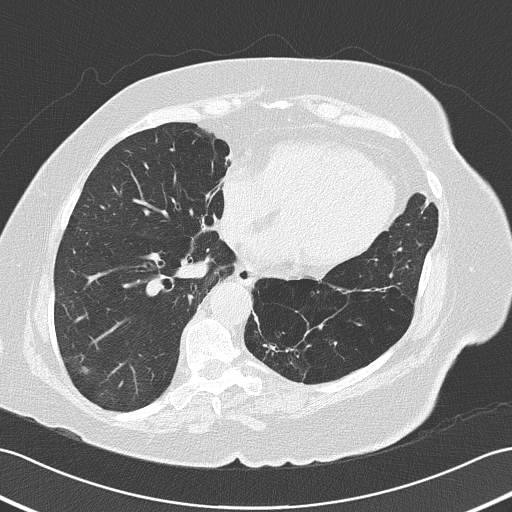
Chest CT (low-dose screening protocol), one axial image, first (baseline) screen, lung window (W 1500 / L -600 HU), 2 mm slice thickness, 512 × 512 image matrix, field of view 353 × 353 mm. Female, age 73 years at enrolment.
- Expert-annotated lung lesion, box from (x=55, y=339) to (x=101, y=388) px.
- The screening reader recorded 4 non-calcified nodules or masses ≥4 mm on this exam (right lower lobe, right upper lobe, left upper lobe, left lower lobe); which of them this box marks is not recorded.
- Official screen result: positive, change unspecified: nodule(s) >= 4 mm or enlarging nodule(s), mass(es), or other non-specific abnormalities suspicious for lung cancer.
- Lung cancer was diagnosed 50 days after this screen: adenocarcinoma, NOS, right lower lobe, poorly differentiated (G3), stage IB (AJCC 6th edition), 17 mm at pathology.